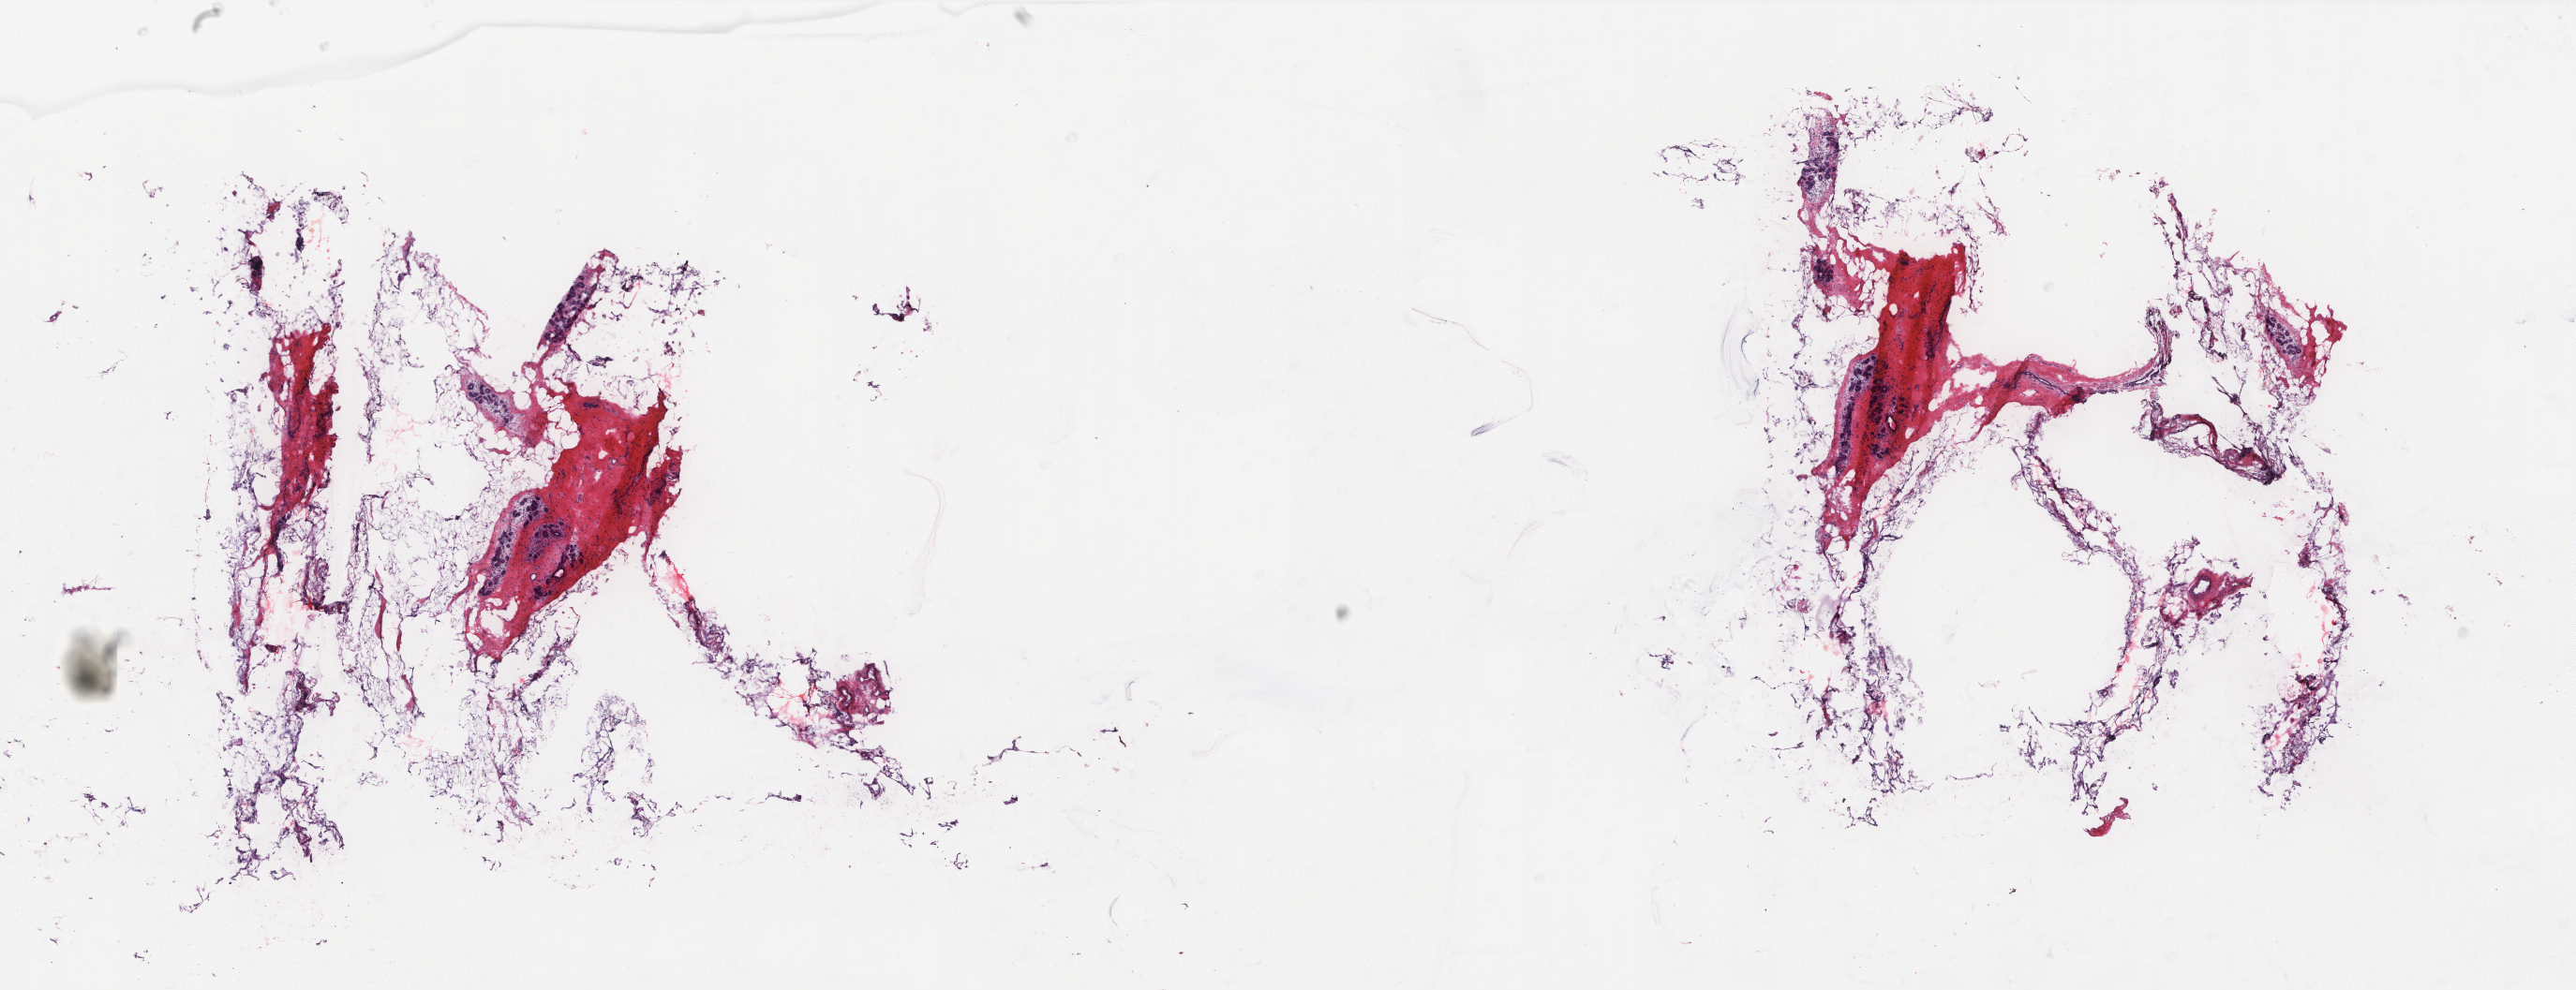
Digitized Hematoxylin and eosin (H&E) stained tissue section (whole slide) — shown as a low-resolution overview of the whole scanned area (about 22.0 x 8.4 mm, acquisition: 20x scan), frozen section from the top of the tissue portion, sample: solid tissue normal (non-tumour tissue), breast. Female patient; age at initial diagnosis 44 years. Pathologist review of this section (percent, as recorded): tumour cells 0%, tumour nuclei 0%, normal cells 30%, stromal cells 70%, necrosis 0%. Infiltration values recorded for this section: lymphocyte infiltration 0%, monocyte infiltration 0%, neutrophil infiltration 0%.
This section: solid tissue normal sample (biorepository sample class). Patient diagnosis: Infiltrating duct carcinoma, NOS.